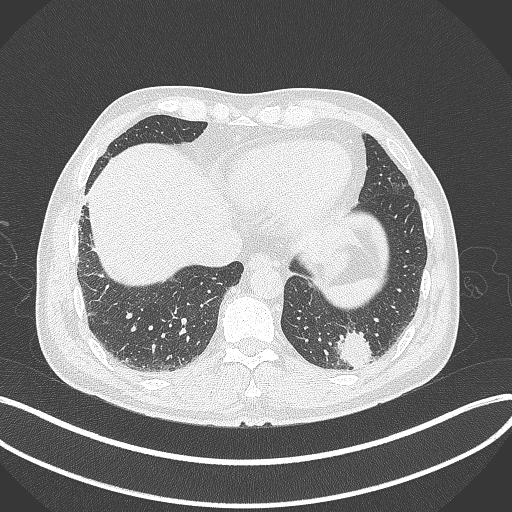
Chest CT, one axial slice; slice 63 of 300 in the series (ordered by position); reconstruction kernel B70f; 120 kVp; lung window (W 1500 / L -600 HU); 1 mm slice thickness; 512 × 512 image matrix, field of view 400 × 400 mm. Patient: male, 54 years. From the clinical record (not read from this slice): clinical TNM (as recorded): T1c N0 M1; histopathological grade: G3.
Structures marked on this image (bounding box drawn by a radiologist):
- lung tumour (recorded histology: adenocarcinoma): bounding box [x1, y1, x2, y2] px = [337, 325, 374, 372]